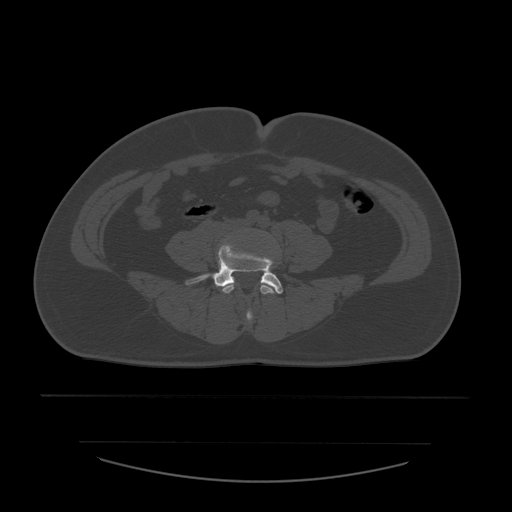
CT including the spine, one axial slice; position 130 of 532 along the scan axis; reconstruction kernel STANDARD; bone window (W 1800 / L 400 HU); 1.25 mm slice thickness; 512 × 512 image matrix, field of view 441 × 441 mm. Patient age 44 years. Case-level facts recorded for this patient, not image findings: primary cancer: soft tissue sarcoma.
Structures marked on this image (semi-automatic segmentation, software-assisted and operator-edited):
- L4 vertebra: bounding box [x1, y1, x2, y2] px = [222, 284, 276, 321]
- L5 vertebra: [187, 245, 283, 294]